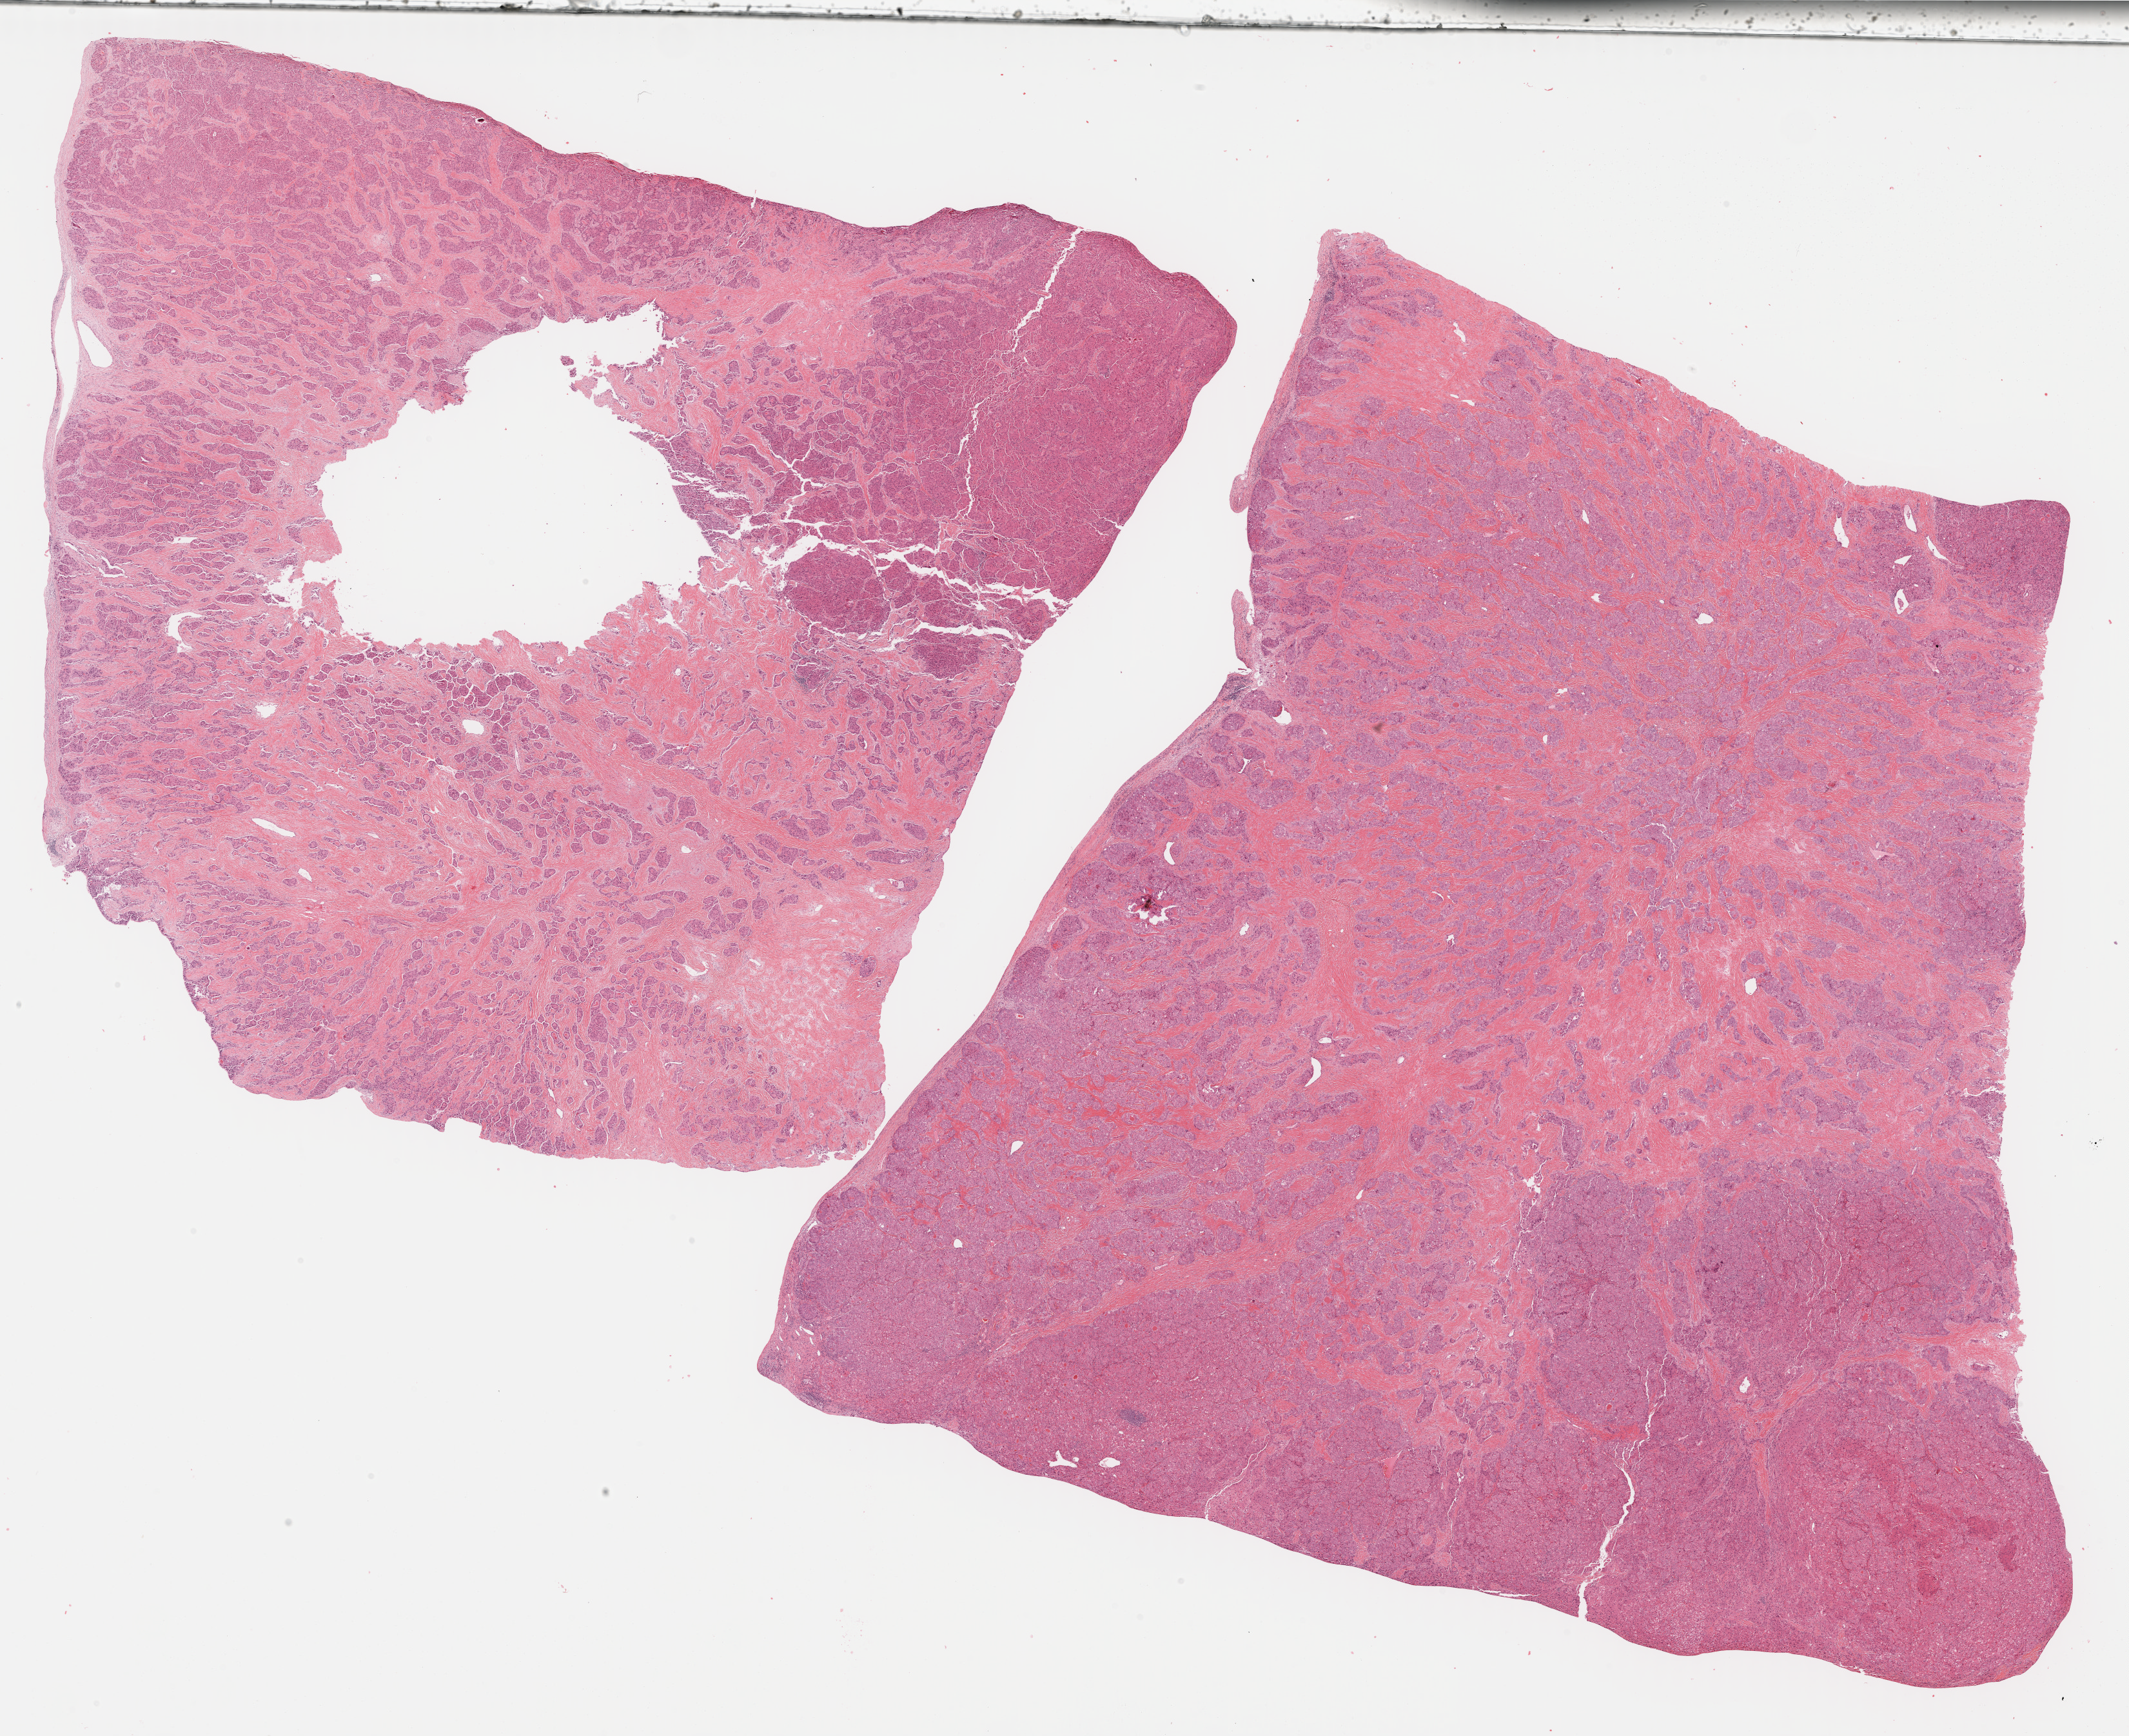
Hematoxylin and eosin (H&E) stained whole-slide image — whole scanned area (about 26.7 x 21.8 mm) shown as a low-resolution overview; formalin-fixed paraffin-embedded (FFPE) diagnostic section; liver, primary tumour sample. Female, age 78 years at initial diagnosis. Histologic grade: G2 (moderately differentiated).
AJCC pathologic stage: I (5th edition). Pathologic diagnosis: Hepatocellular carcinoma, NOS. TNM: T1 NX M0.